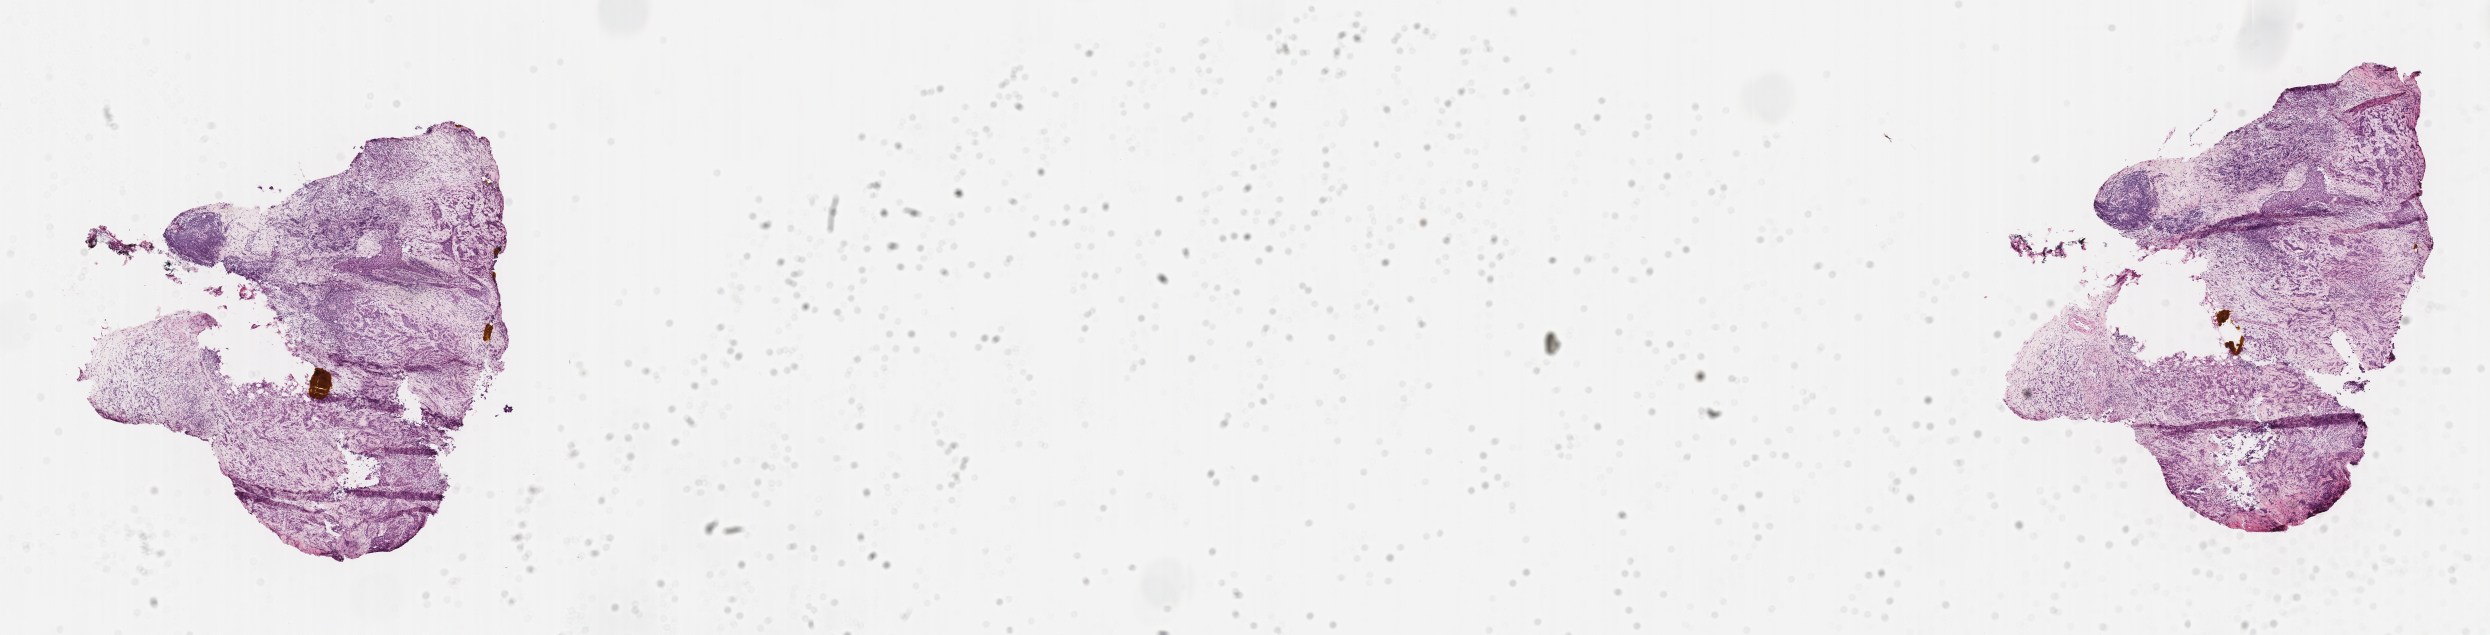
Whole-slide image, haematoxylin and eosin stain, shown as a low-resolution overview of the whole scanned area (about 20.1 x 5.1 mm). Cryosection. Primary tumor. Site: breast (right). Patient: female, age at initial diagnosis 69 years.
Histologic diagnosis: Infiltrating duct carcinoma, NOS.